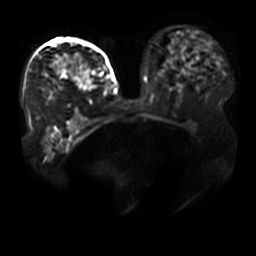
Breast MRI, one axial slice. Slice 27 of 41 in the series (ordered by position). Diffusion-weighted series; image 2 of 4 stored at this slice position (different b-values; order by instance number). 3 T. 256 × 256 image matrix. Female patient.
Structures marked on this image (manually delineated by an expert):
- tumour on diffusion-weighted imaging: box from (x=66, y=56) to (x=94, y=90) px